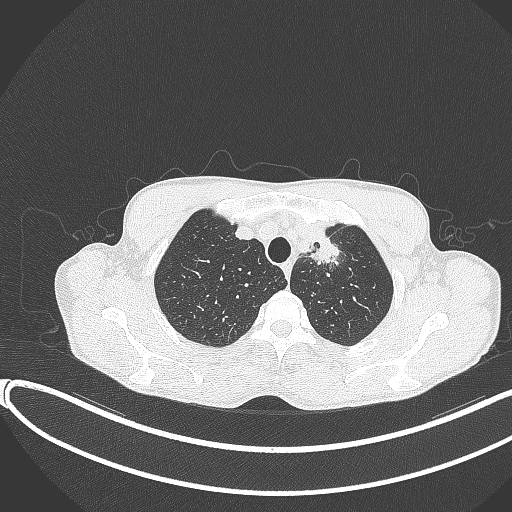
Chest CT, one axial slice. Position 327 of 374 along the scan axis. Lung window (W 1500 / L -600 HU). 1 mm slice thickness. 512 × 512 image matrix, field of view 400 × 400 mm. Male patient, age 58 years. From the clinical record (not read from this slice): clinical TNM (as recorded): T1c N1 M0.
Structures marked on this image (rectangle marked by the reading radiologist):
- lung tumour (recorded histology: adenocarcinoma): bounding box [x1, y1, x2, y2] px = [304, 224, 340, 269]